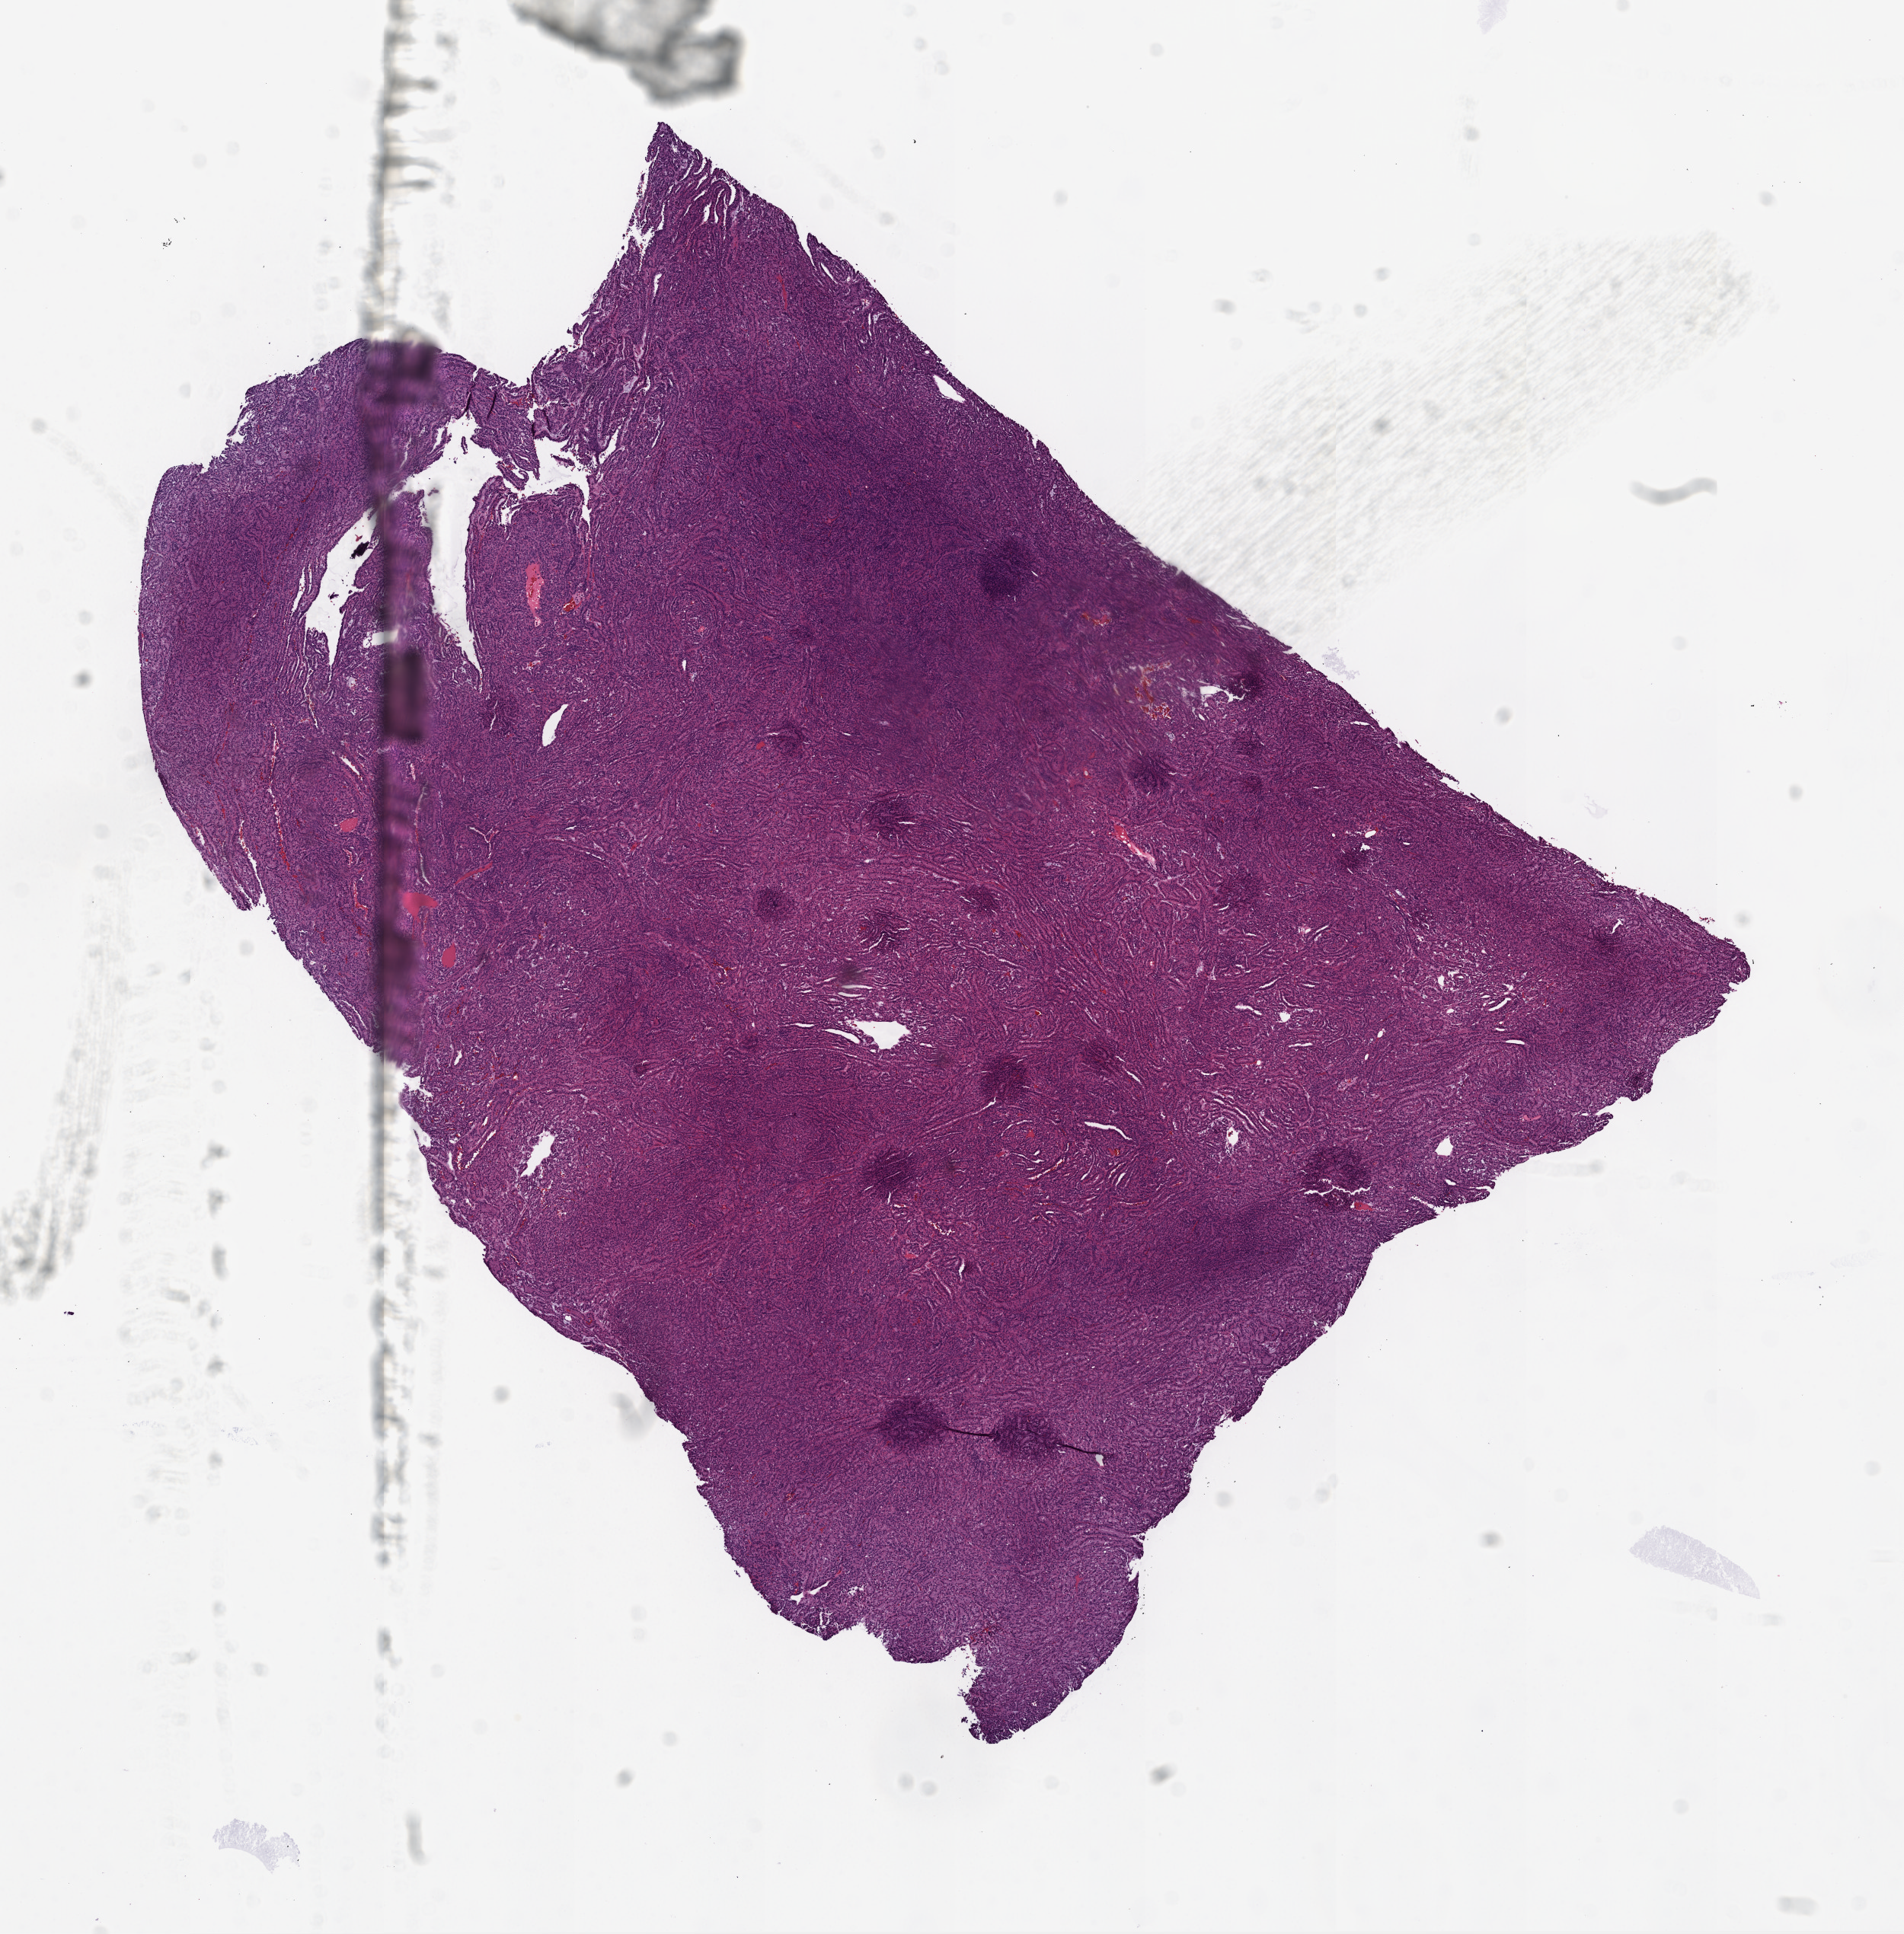
H&E-stained whole-slide image, low-resolution overview of the scanned area, about 10.0 x 10.2 mm (from a 20x scan). Frozen section from the top of the tissue portion. Primary tumour sample from the kidney. Female, age 59 years at initial diagnosis. Composition of this section per pathologist review: tumour cells 98%, tumour nuclei 90%, normal cells 0%, stromal cells 2%, necrosis 0%.
Diagnosis: Papillary adenocarcinoma, NOS. TNM: T1 NX M0. AJCC pathologic stage: I.